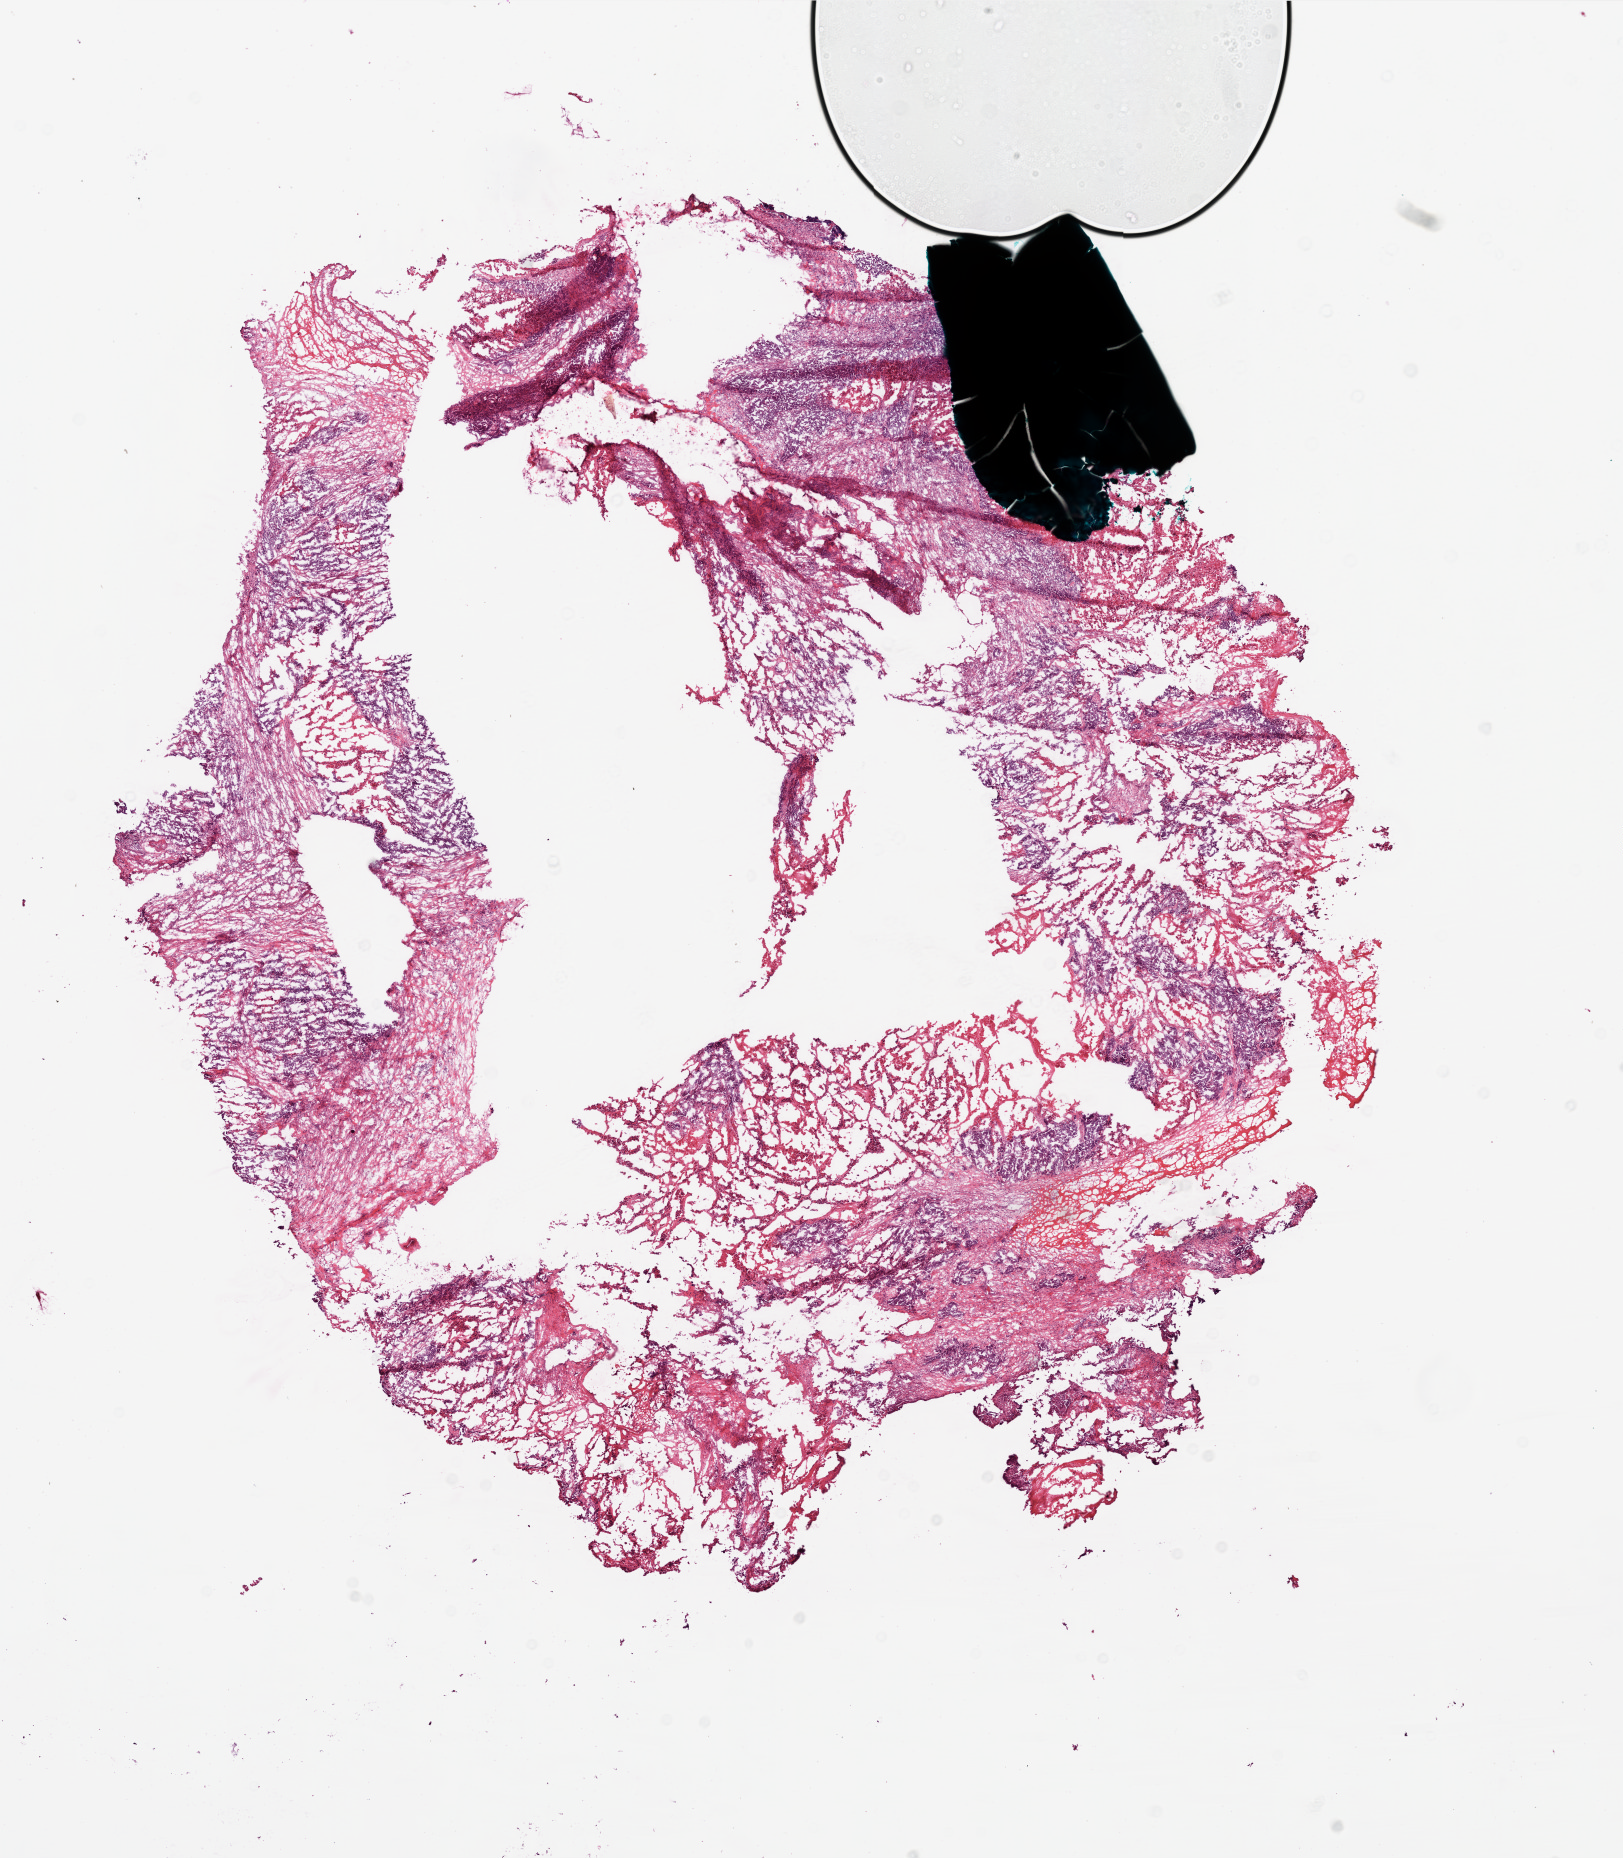
Whole-slide histology image, H&E, a low-resolution overview of the entire scanned area, about 13.0 x 14.9 mm (from a 20x scan), frozen section, sample: primary tumour, ovary. Female patient; age at initial diagnosis 54 years. Histologic grade: G3 (poorly differentiated). Slide review estimates, as recorded: tumour cells 75%, tumour nuclei 80%, normal cells 0%, stromal cells 20%, necrosis 5%. Inflammatory infiltration, as recorded: lymphocyte infiltration 100%.
* FIGO stage: IIIC
* pathologic diagnosis: Serous cystadenocarcinoma, NOS